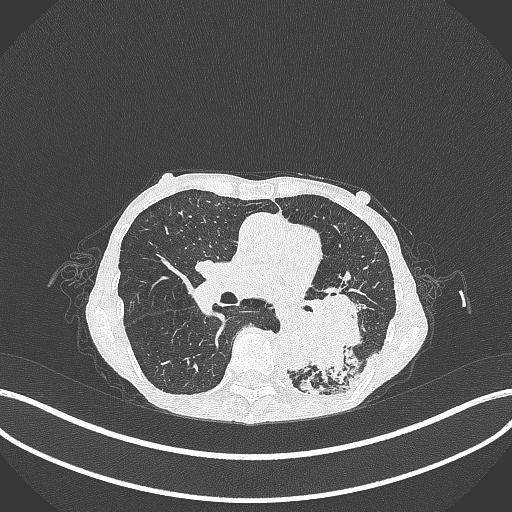
Chest CT, one axial slice. Position 142 of 347 along the scan axis. Reconstruction kernel B70f. 120 kVp. Lung window (W 1500 / L -600 HU). 512 × 512 image matrix. Patient: female, 70 years. Case-level facts recorded for this patient, not image findings: clinical TNM (as recorded): T3 N0 M0.
Structures marked on this image (rectangle marked by the reading radiologist):
- lung tumour (recorded histology: small cell carcinoma): bounding box (x1, y1, x2, y2) in pixels: (289, 286, 375, 393)